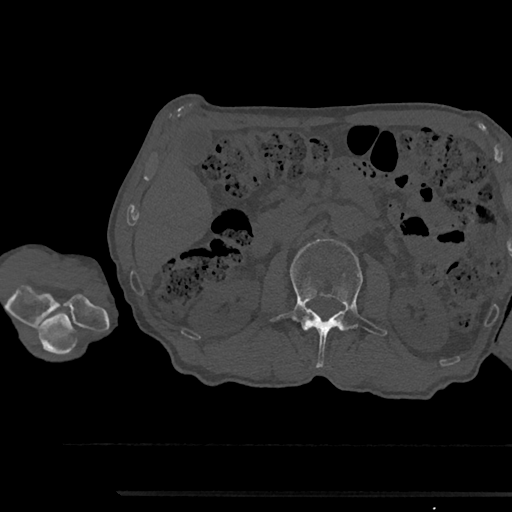
CT including the spine, one axial slice; position 568 of 797 along the scan axis; reconstruction kernel Br40s/3; 120 kVp; bone window (W 1800 / L 400 HU); 0.5 mm slice thickness; 512 × 512 image matrix, field of view 367 × 367 mm. Patient: male, 79 years. Case-level facts recorded for this patient, not image findings: primary cancer: prostate.
Structures marked on this image (semi-automatic segmentation, software-assisted and operator-edited):
- L2 vertebra: bounding box (x1, y1, x2, y2) in pixels: (270, 239, 387, 368)